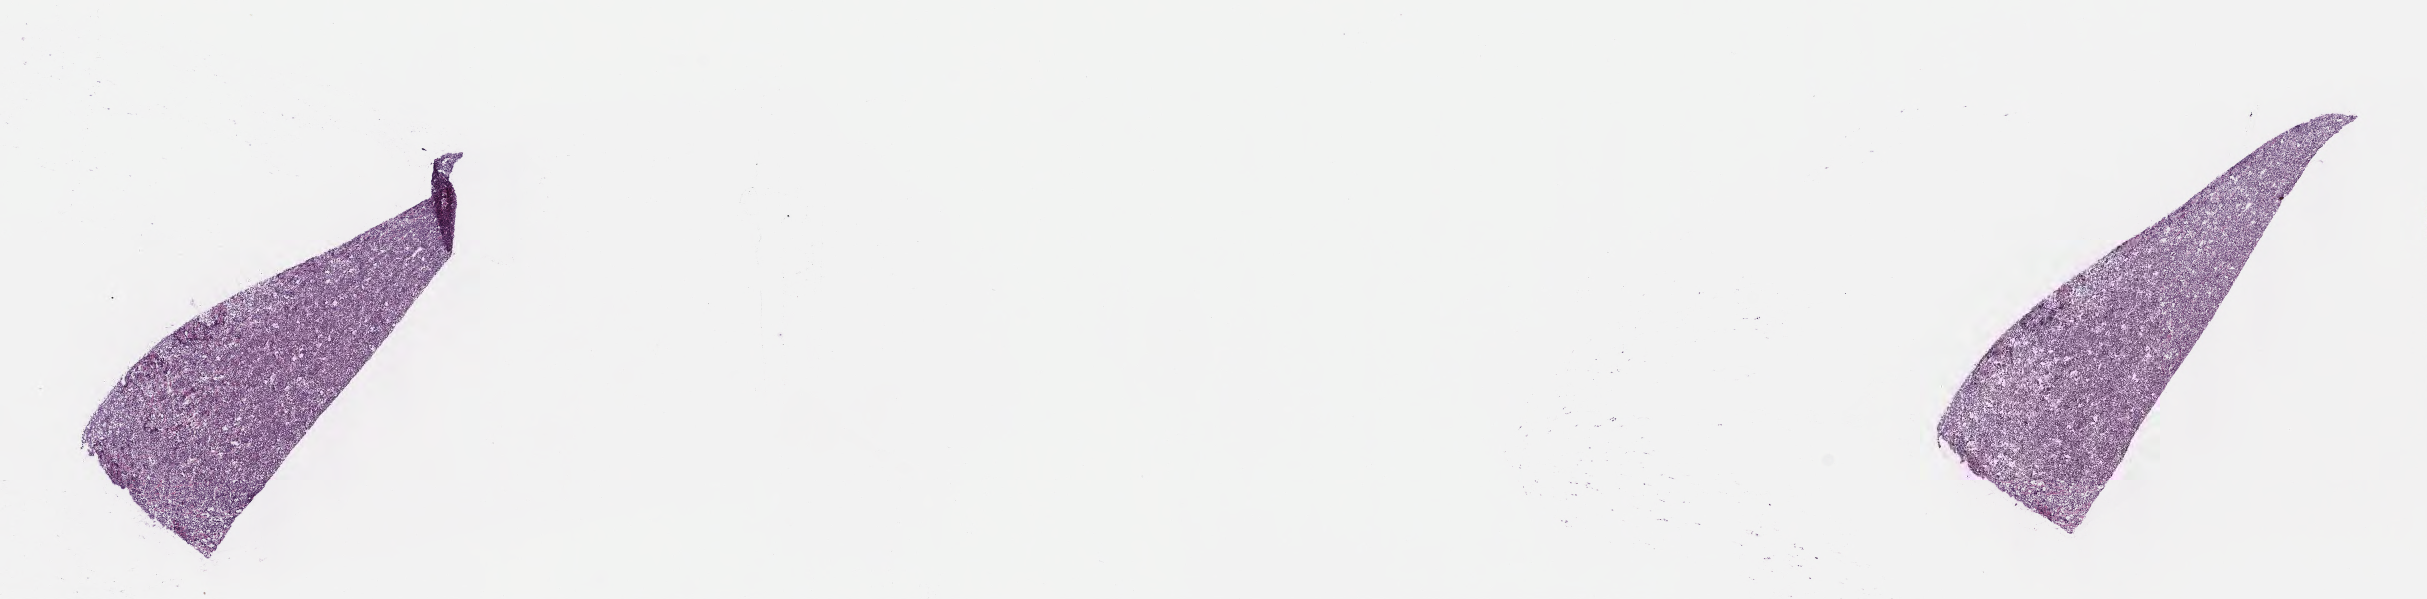
H&E whole-slide image, shown as a low-resolution overview of the whole scanned area (about 19.6 x 4.8 mm). Cryosection. Specimen: primary tumor. Site: cranium. Male, age 5 years at initial diagnosis. Pathologist review of this section (percent, as recorded): tumor cells 90%, tumor nuclei 90%, stromal cells 5%, necrosis 0%, normal cells 5%. Infiltration values recorded for this section: lymphocyte infiltration 80%, monocyte infiltration 5%, neutrophil infiltration 5%.
Ann Arbor stage (patient): Stage IV. Histologic diagnosis: Burkitt lymphoma, NOS.